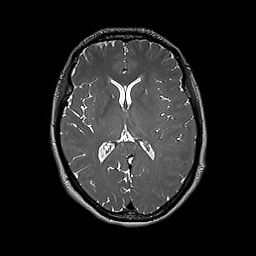
Brain MRI from a brain-tumour surgery series, one axial slice; position 99 of 192 along the scan axis; 1 mm slice thickness; 256 × 256 image matrix. Case-level facts recorded for this patient, not image findings: histopathology: Glioblastoma; WHO grade: 4; IDH mutation: no; tumour location: Left Frontal.
Structures marked on this image (expert manual segmentation):
- tumour: box from (x=178, y=164) to (x=187, y=167) px